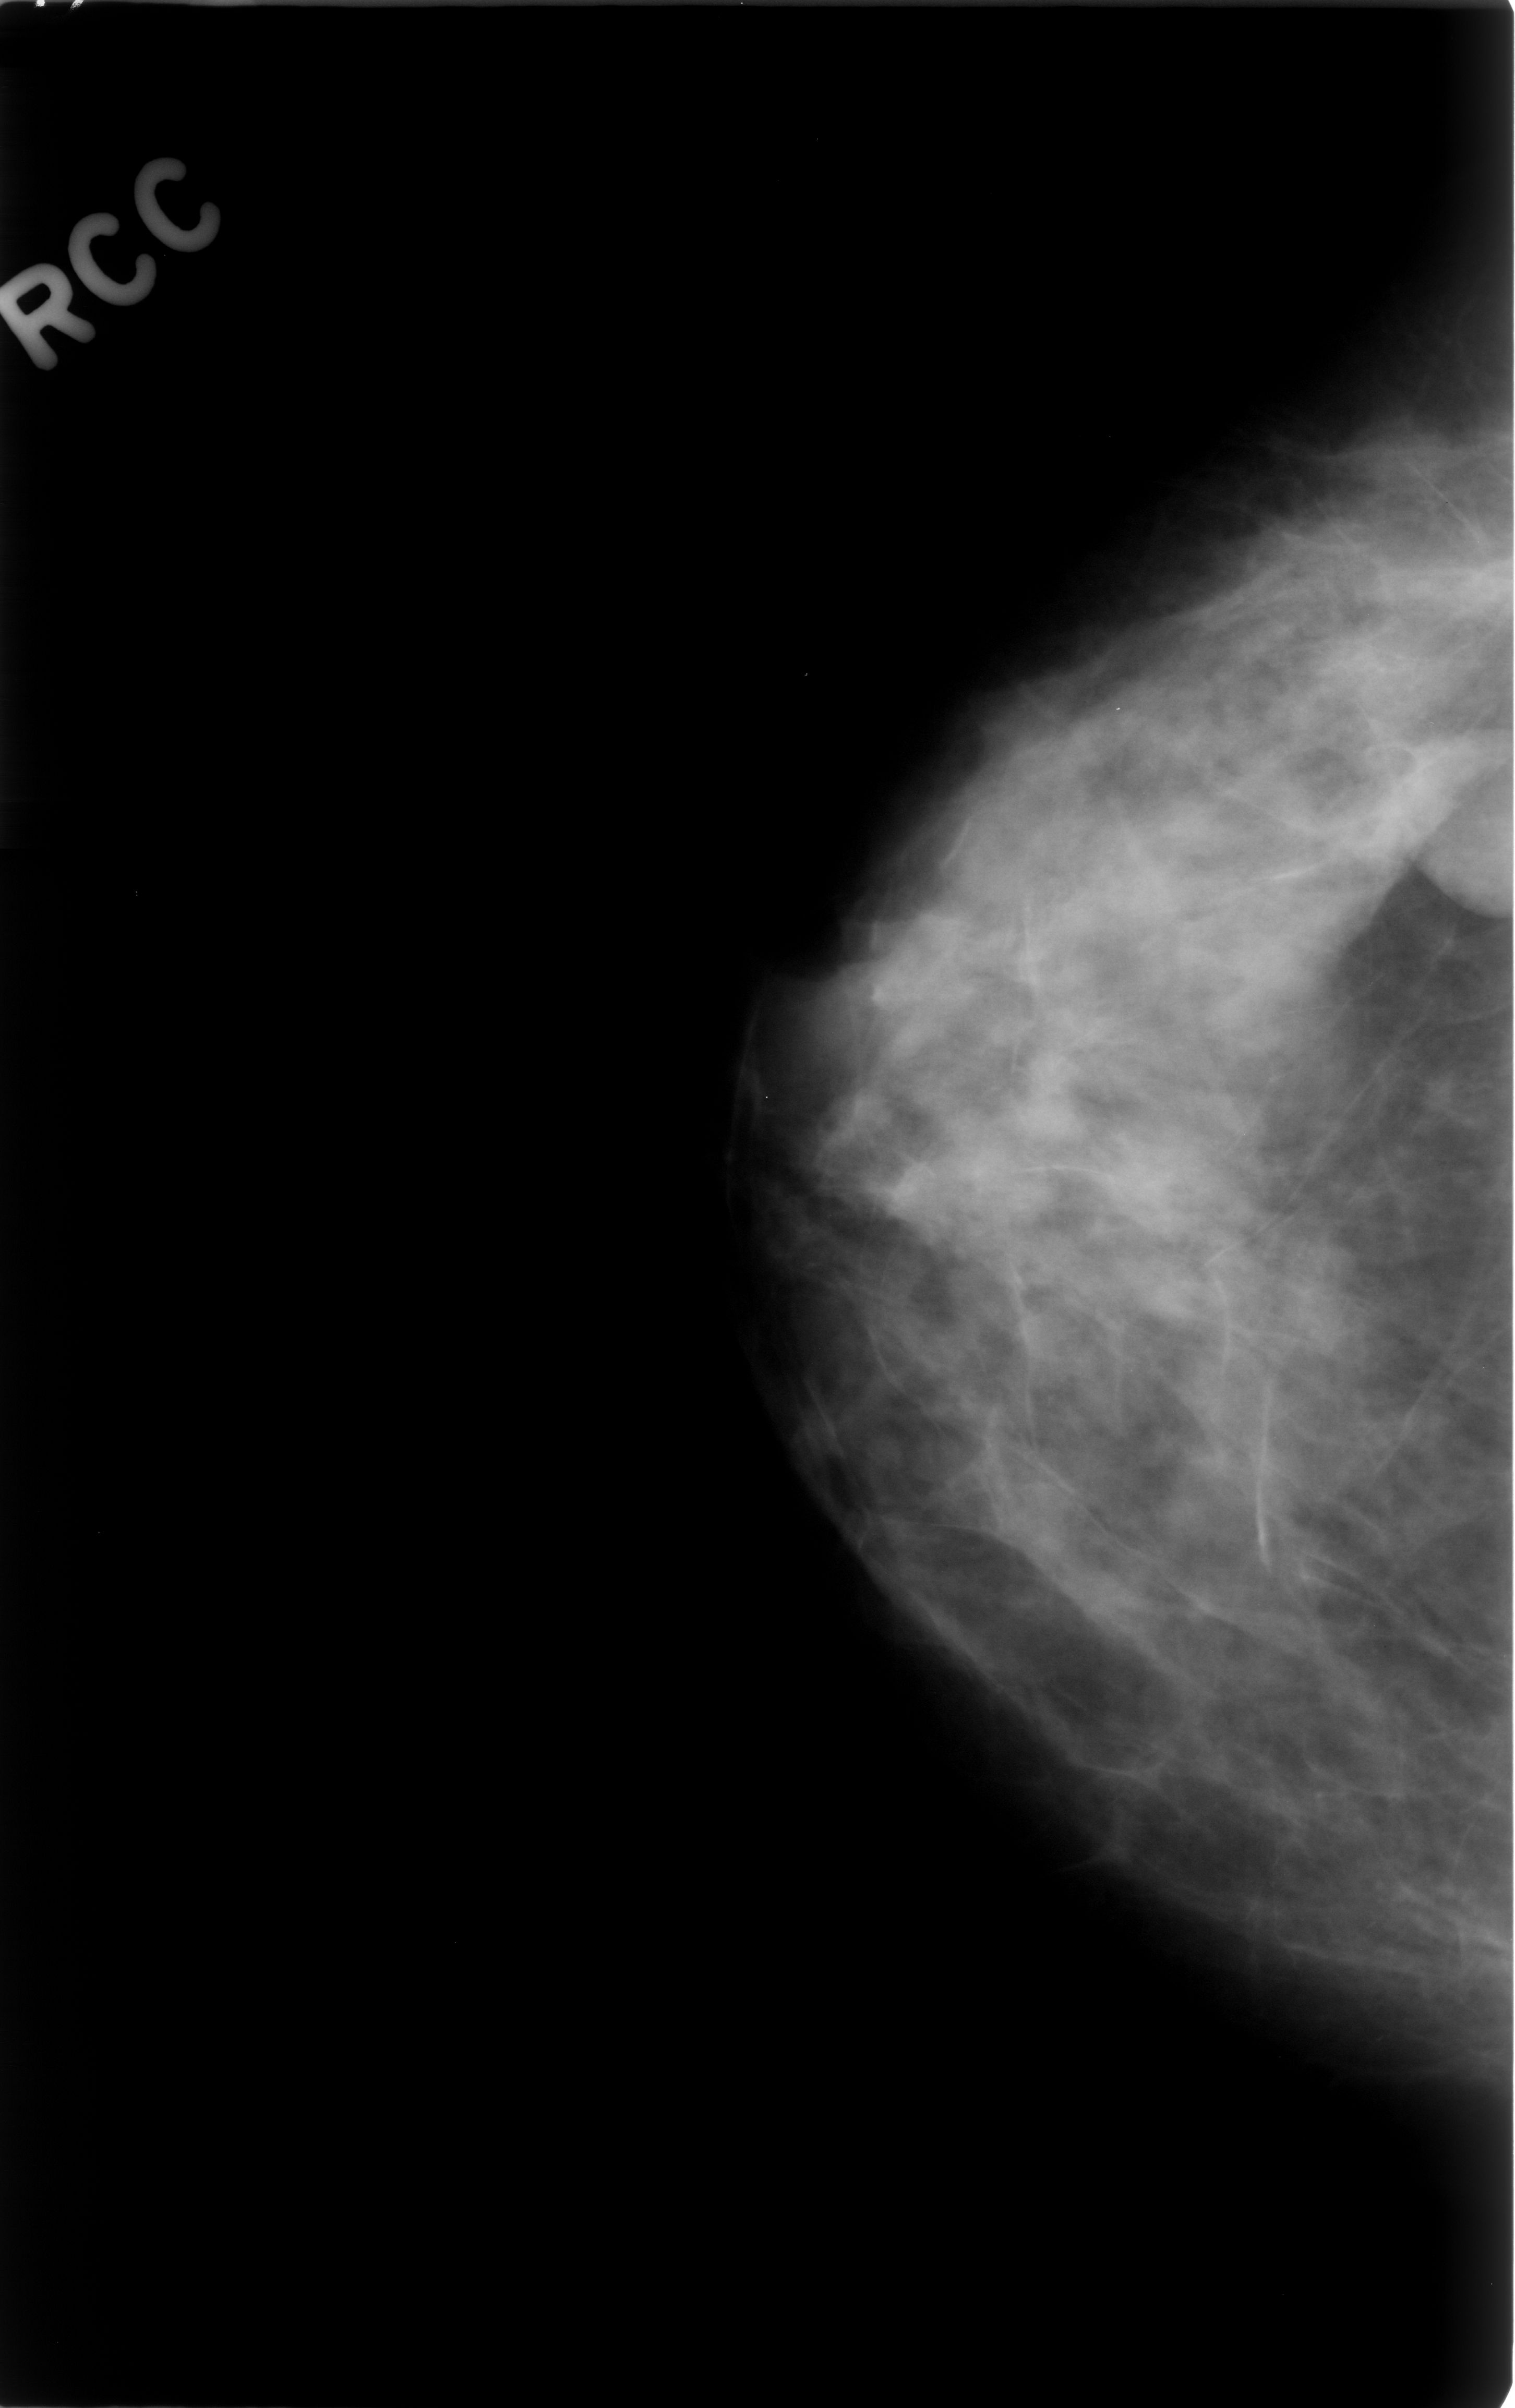
Mammogram (digitized film), right breast, CC view.
Marked abnormality: mass, shape round, margins circumscribed; BI-RADS assessment category 3; subtlety rating 4 on a 1 (subtle) to 5 (obvious) scale; pathology result (as recorded, not read from the image): benign.